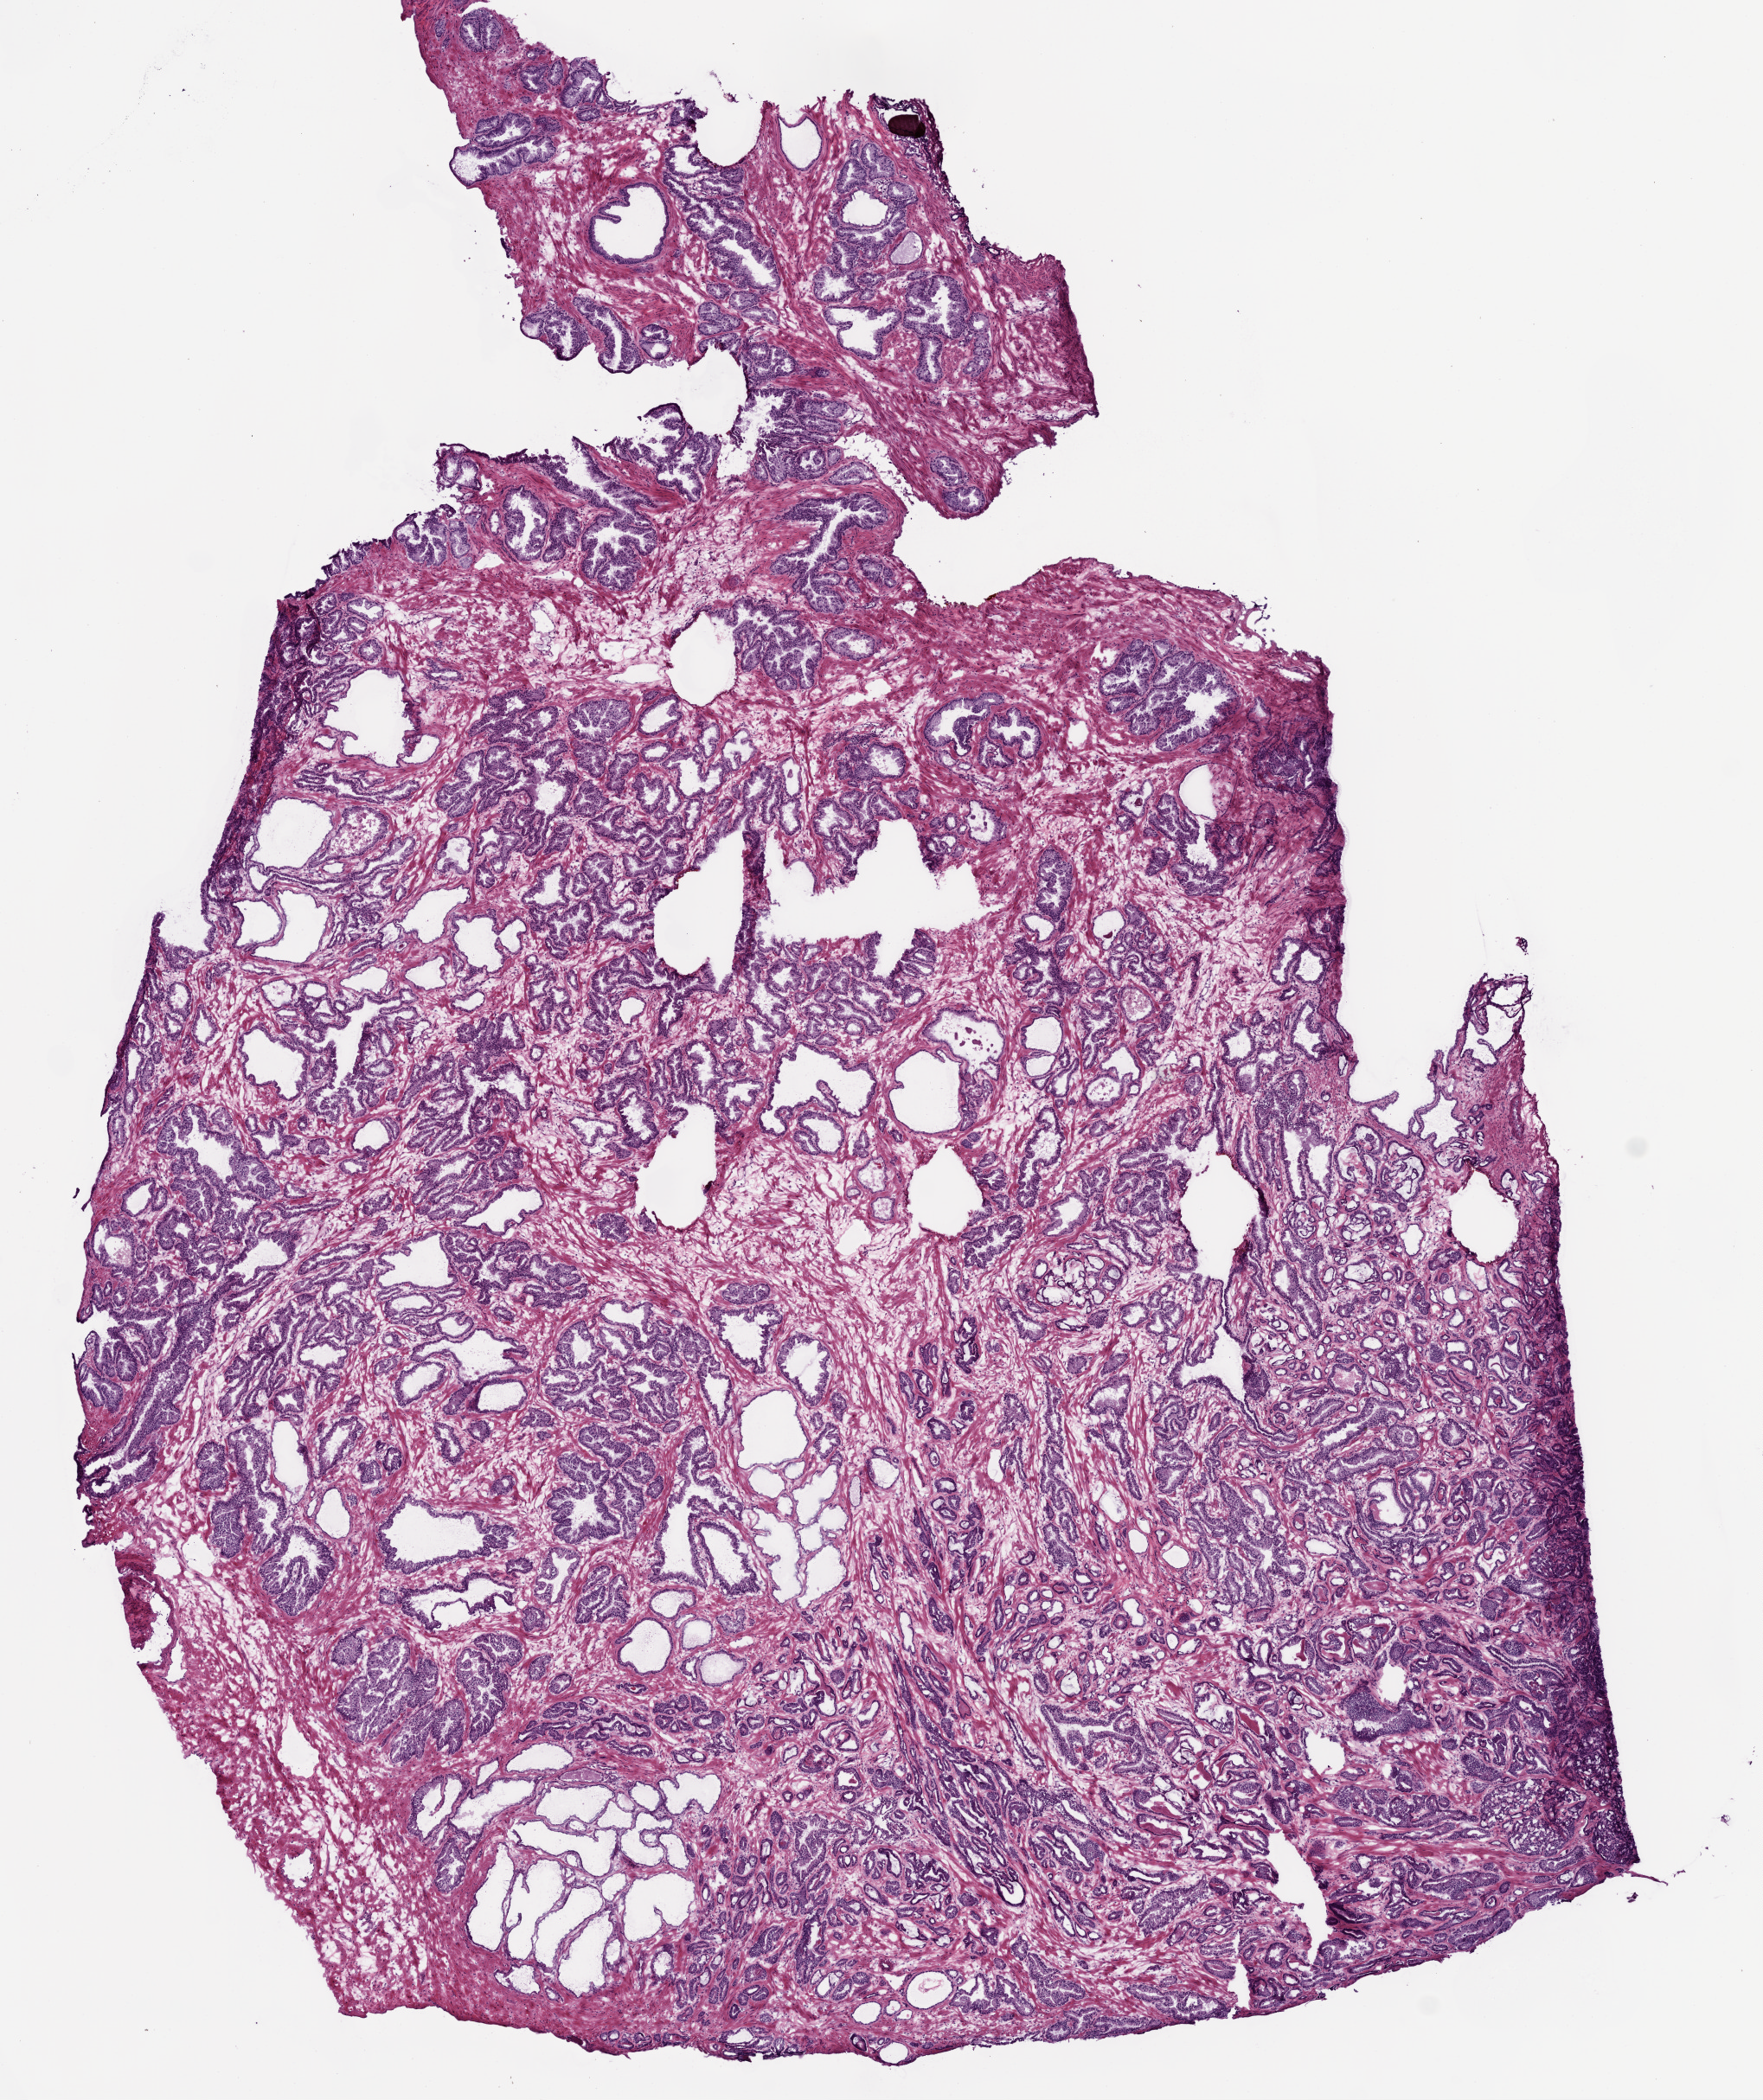
Digitized H&E-stained tissue section (whole slide), low-resolution overview of the scanned area, about 8.2 x 9.8 mm, frozen section, primary tumour sample from the prostate. Male patient; age at initial diagnosis 49 years. Gleason score: 7 (3+4). Composition of this section per pathologist review: tumour cells 85%, tumour nuclei 85%, normal cells 5%, stromal cells 10%, necrosis 0%.
Histologic diagnosis: Acinar cell carcinoma. Laterality: bilateral.